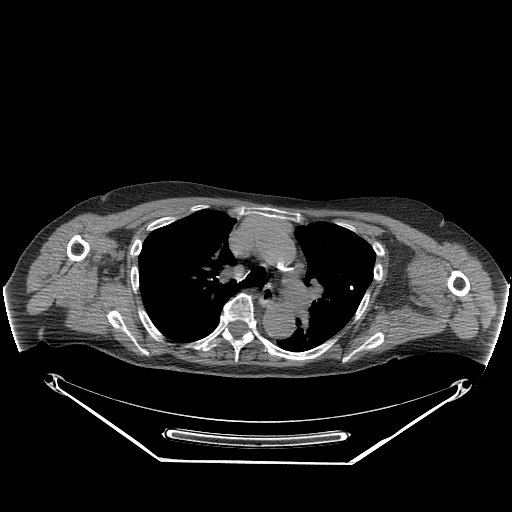
CT of an extremity soft-tissue mass (from a PET/CT study), one axial slice; slice 186 of 267 in the series (ordered by position); 140 kVp; soft-tissue window (W 400 / L 40 HU); 3.75 mm slice thickness; 512 × 512 image matrix. Female patient. Case-level facts recorded for this patient, not image findings: histological type: pleiomorphic leiomyosarcoma; grade: high; site of the primary tumour: left biceps.
Outlined on this slice (expert contour drawn on MRI and transferred to this co-registered scan by the dataset authors):
- gross tumour volume including surrounding oedema: box from (x=411, y=256) to (x=439, y=302) px
- gross tumour volume (mass): (x=420, y=267)–(x=435, y=282)